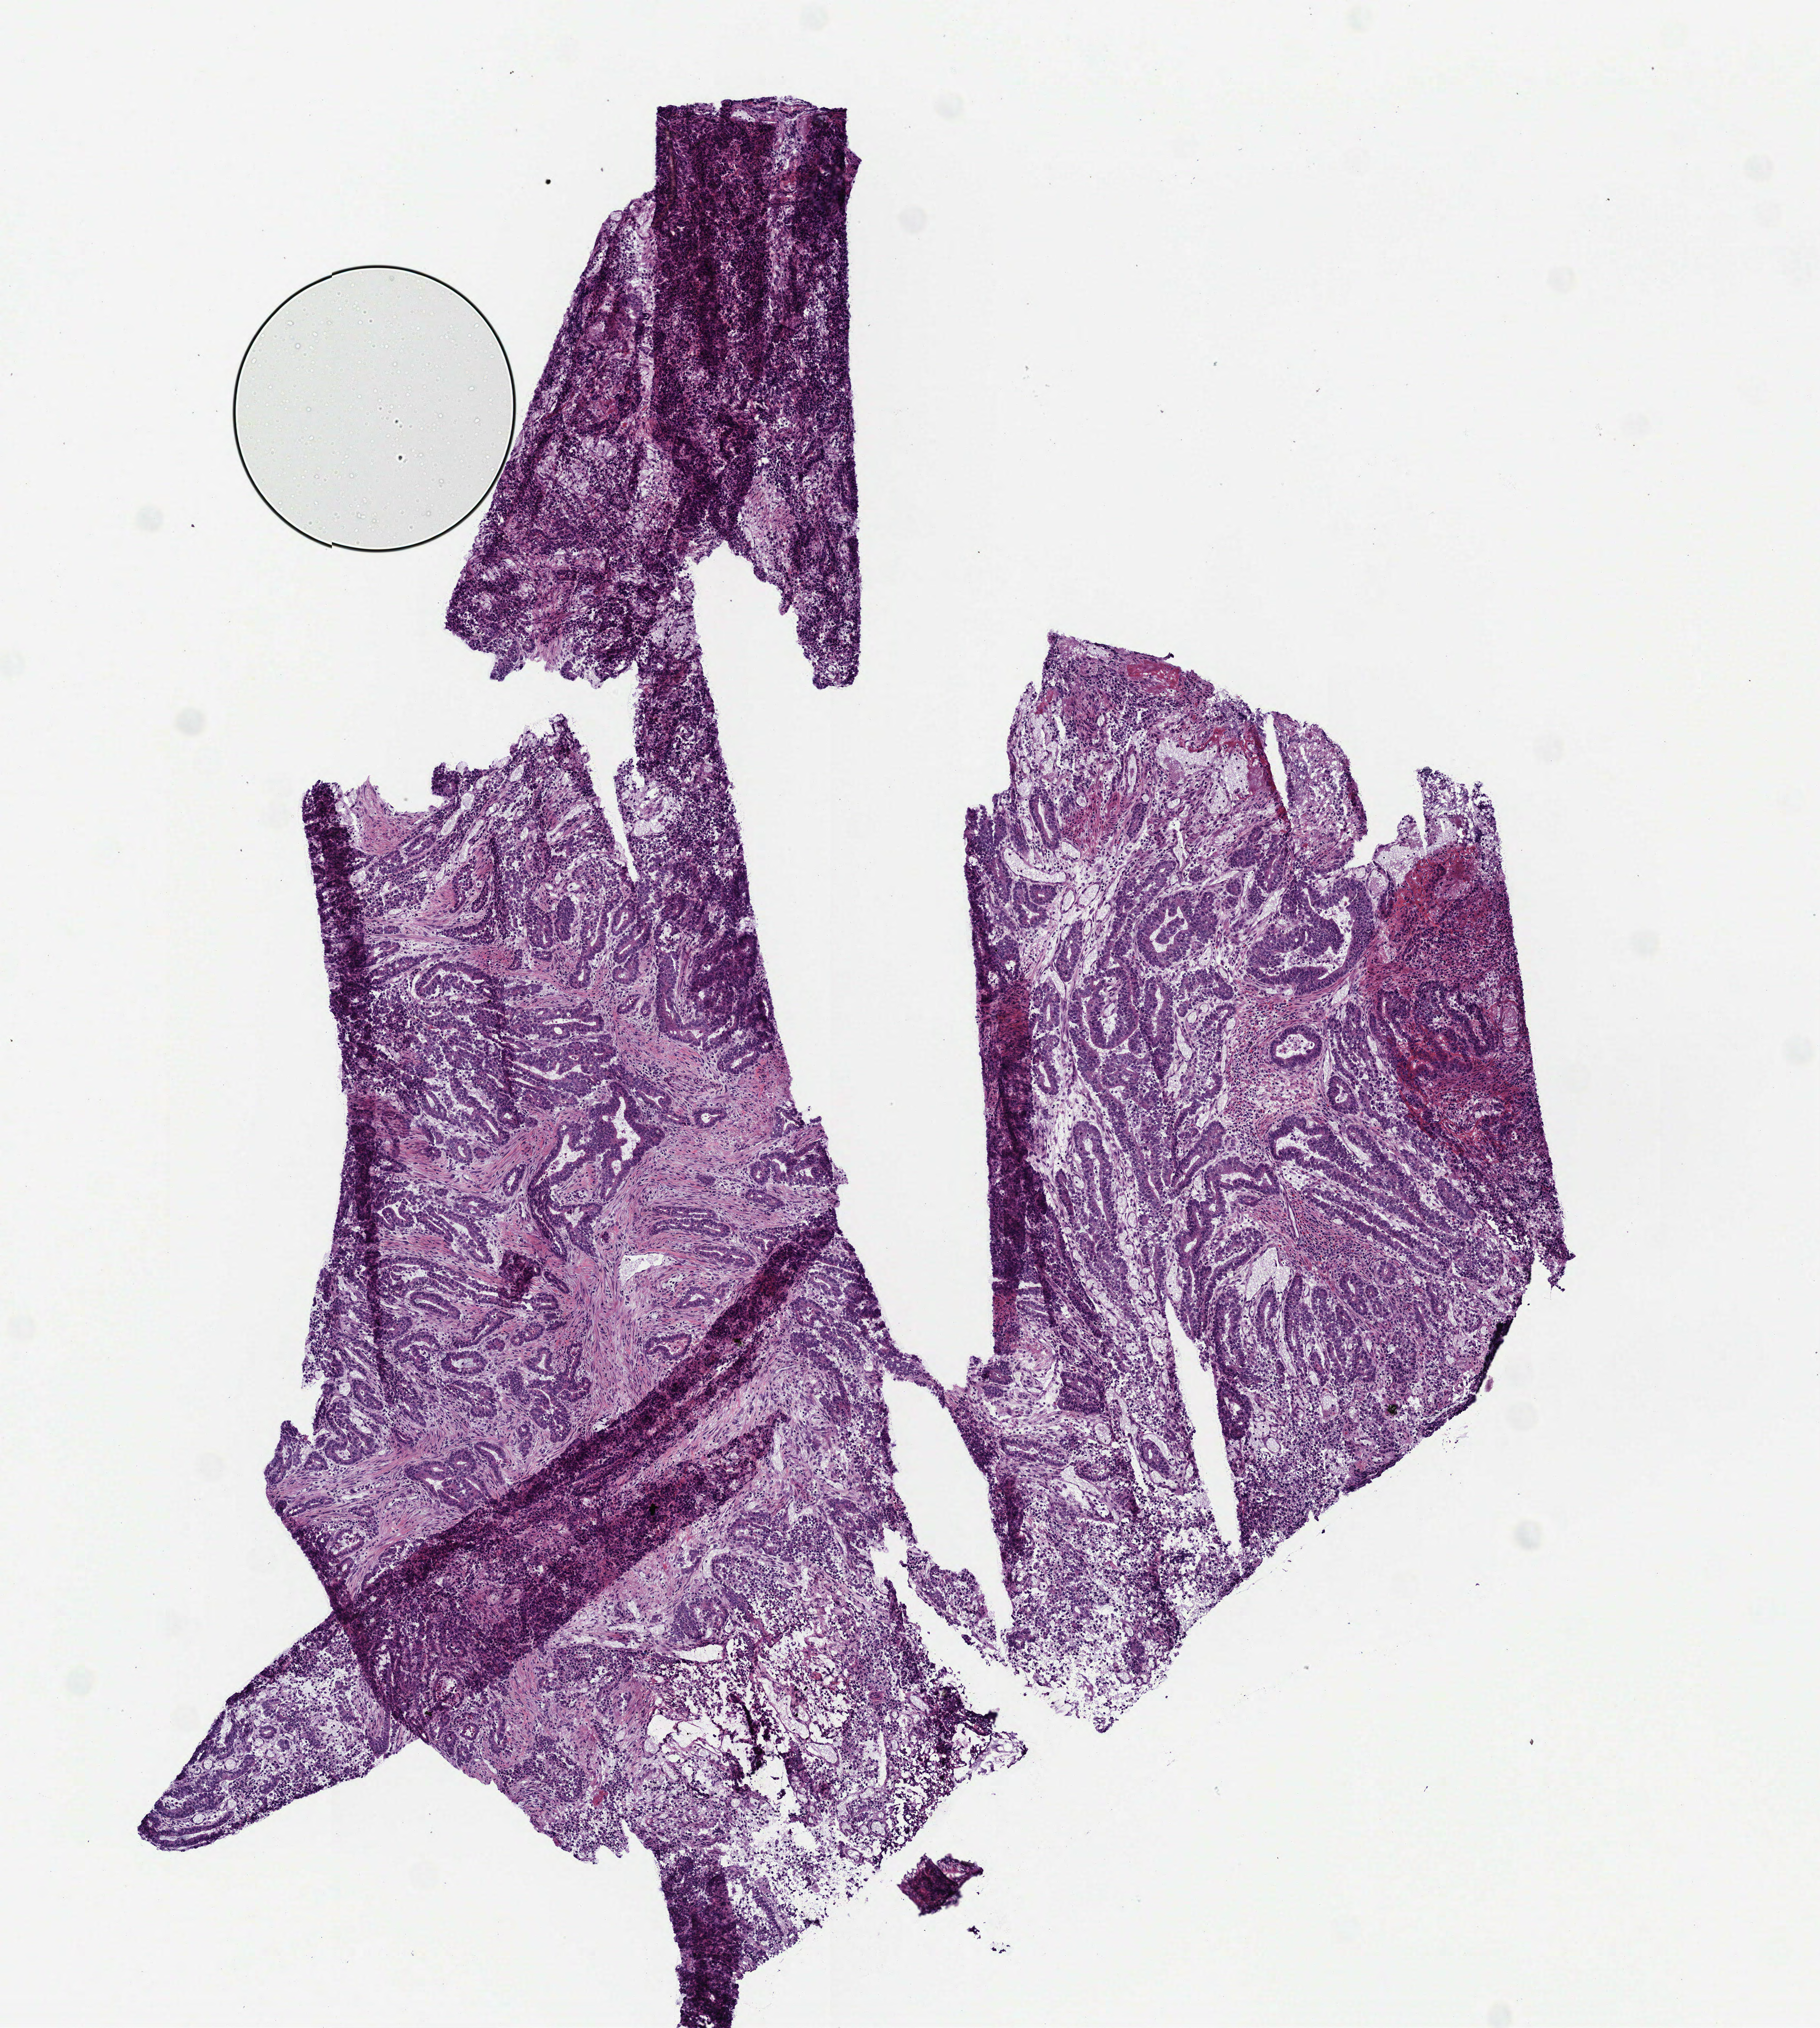
H&E whole-slide image, whole scanned area (about 5.5 x 6.2 mm, acquisition: 40x scan) shown as a low-resolution overview. Frozen section from the bottom of the tissue portion. Primary tumour sample from the stomach. Male patient; age at initial diagnosis 74 years. Histologic grade: G2 (moderately differentiated). Slide review estimates, as recorded: tumour cells 100%, tumour nuclei 80%, normal cells 0%, stromal cells 0%, necrosis 0%. Inflammatory infiltration, as recorded: lymphocyte infiltration 8%, monocyte infiltration 0%, neutrophil infiltration 8%.
Lymph nodes positive (case pathology): 4 of 49 examined. Histologic diagnosis: Signet ring cell carcinoma (cardia, NOS). AJCC pathologic stage: IIIB.